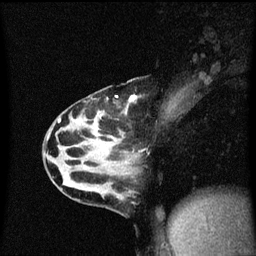
Breast MRI (dynamic contrast-enhanced), one sagittal slice. Position 25 of 60 along the scan axis. Dynamic contrast-enhanced series, image 2 of 3 at this slice position (ordered by acquisition). 1.5 T. TE 4.2 ms, TR 8.4 ms. 256 × 256 image matrix, field of view 200 × 200 mm. Patient: female, 32 years.
Structures marked on this image (semi-automatically segmented with operator editing):
- analysis volume of interest (the breast-tissue region the enhancement analysis was run in; not a lesion): bounding box [x1, y1, x2, y2] px = [55, 80, 171, 167]
- tumour enhancement mask (voxels above the 70 % enhancement threshold inside the analysis volume of interest): [59, 96, 137, 165]